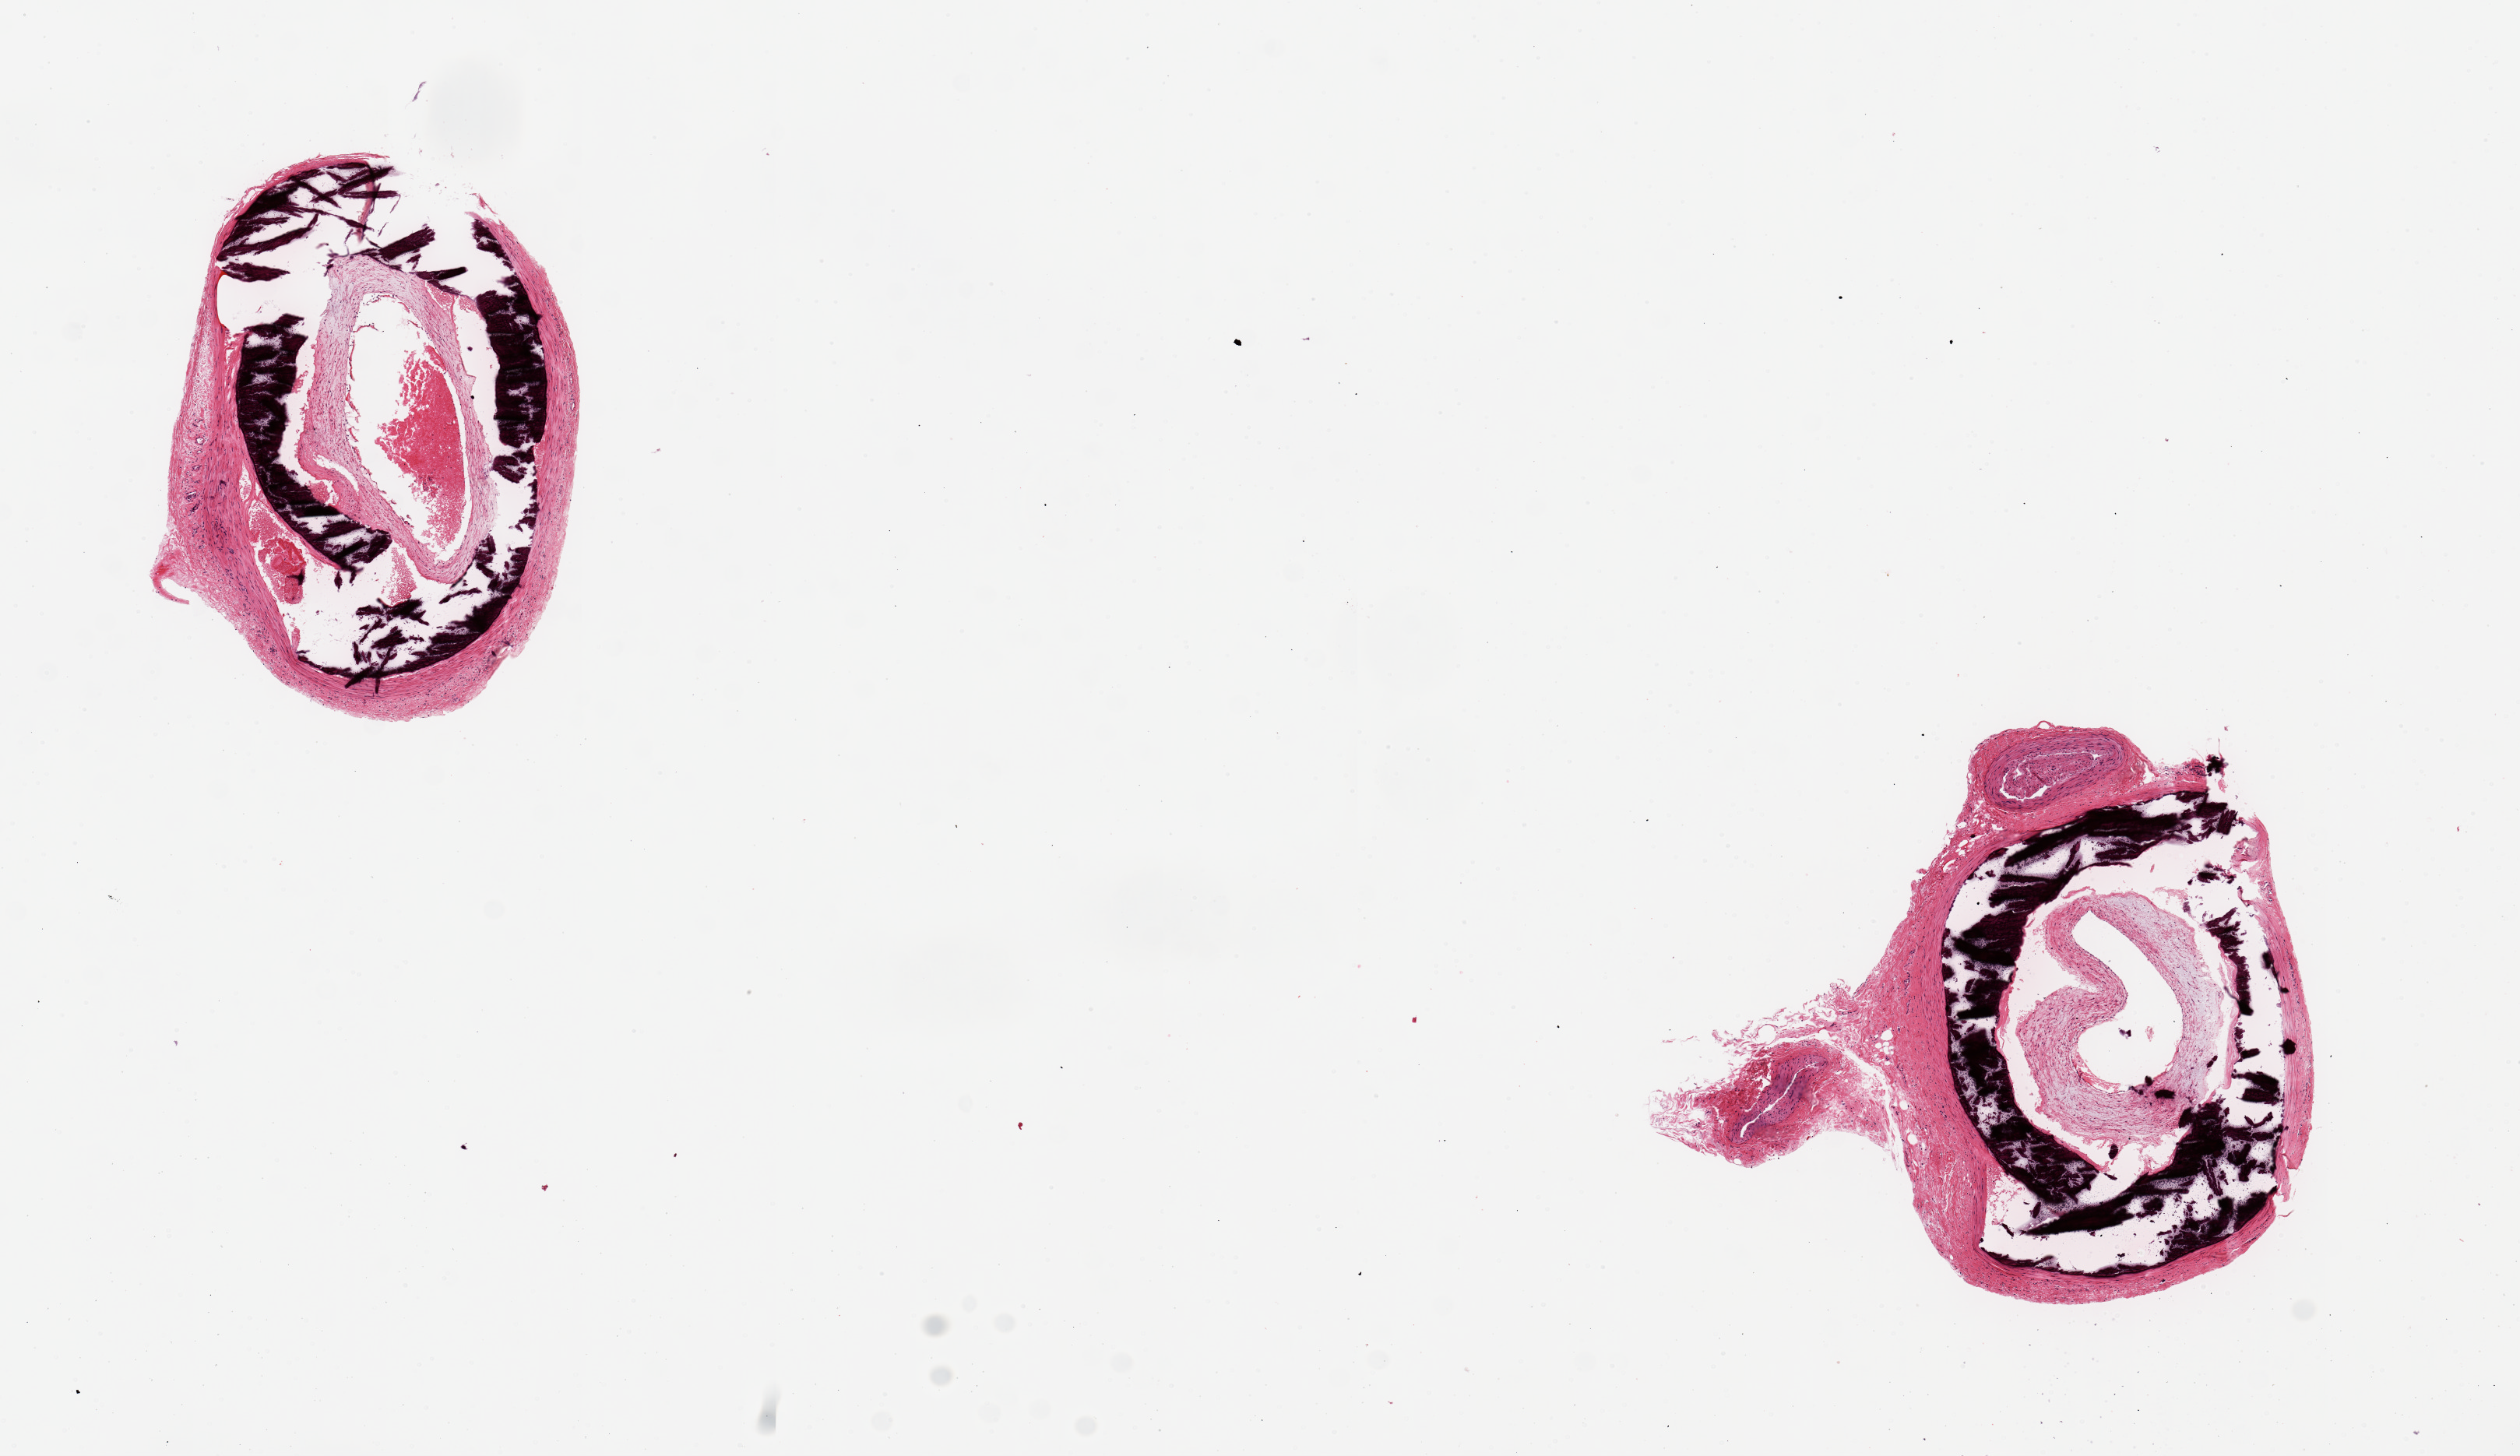
Whole-slide image, H&E stain — shown as a low-resolution overview of the whole scanned area (about 12.8 x 7.4 mm, acquisition: 20x scan). PAXgene-fixed, paraffin-embedded tissue. Target tissue: tibial artery. Tissue donor sample. Donor: male.
Pathologist's review note for this sample: 2 pieces, 3x2 & 3x3mm; severe medial calcification; a small 0.7mm artery (and vein) nearby are free of lesions.